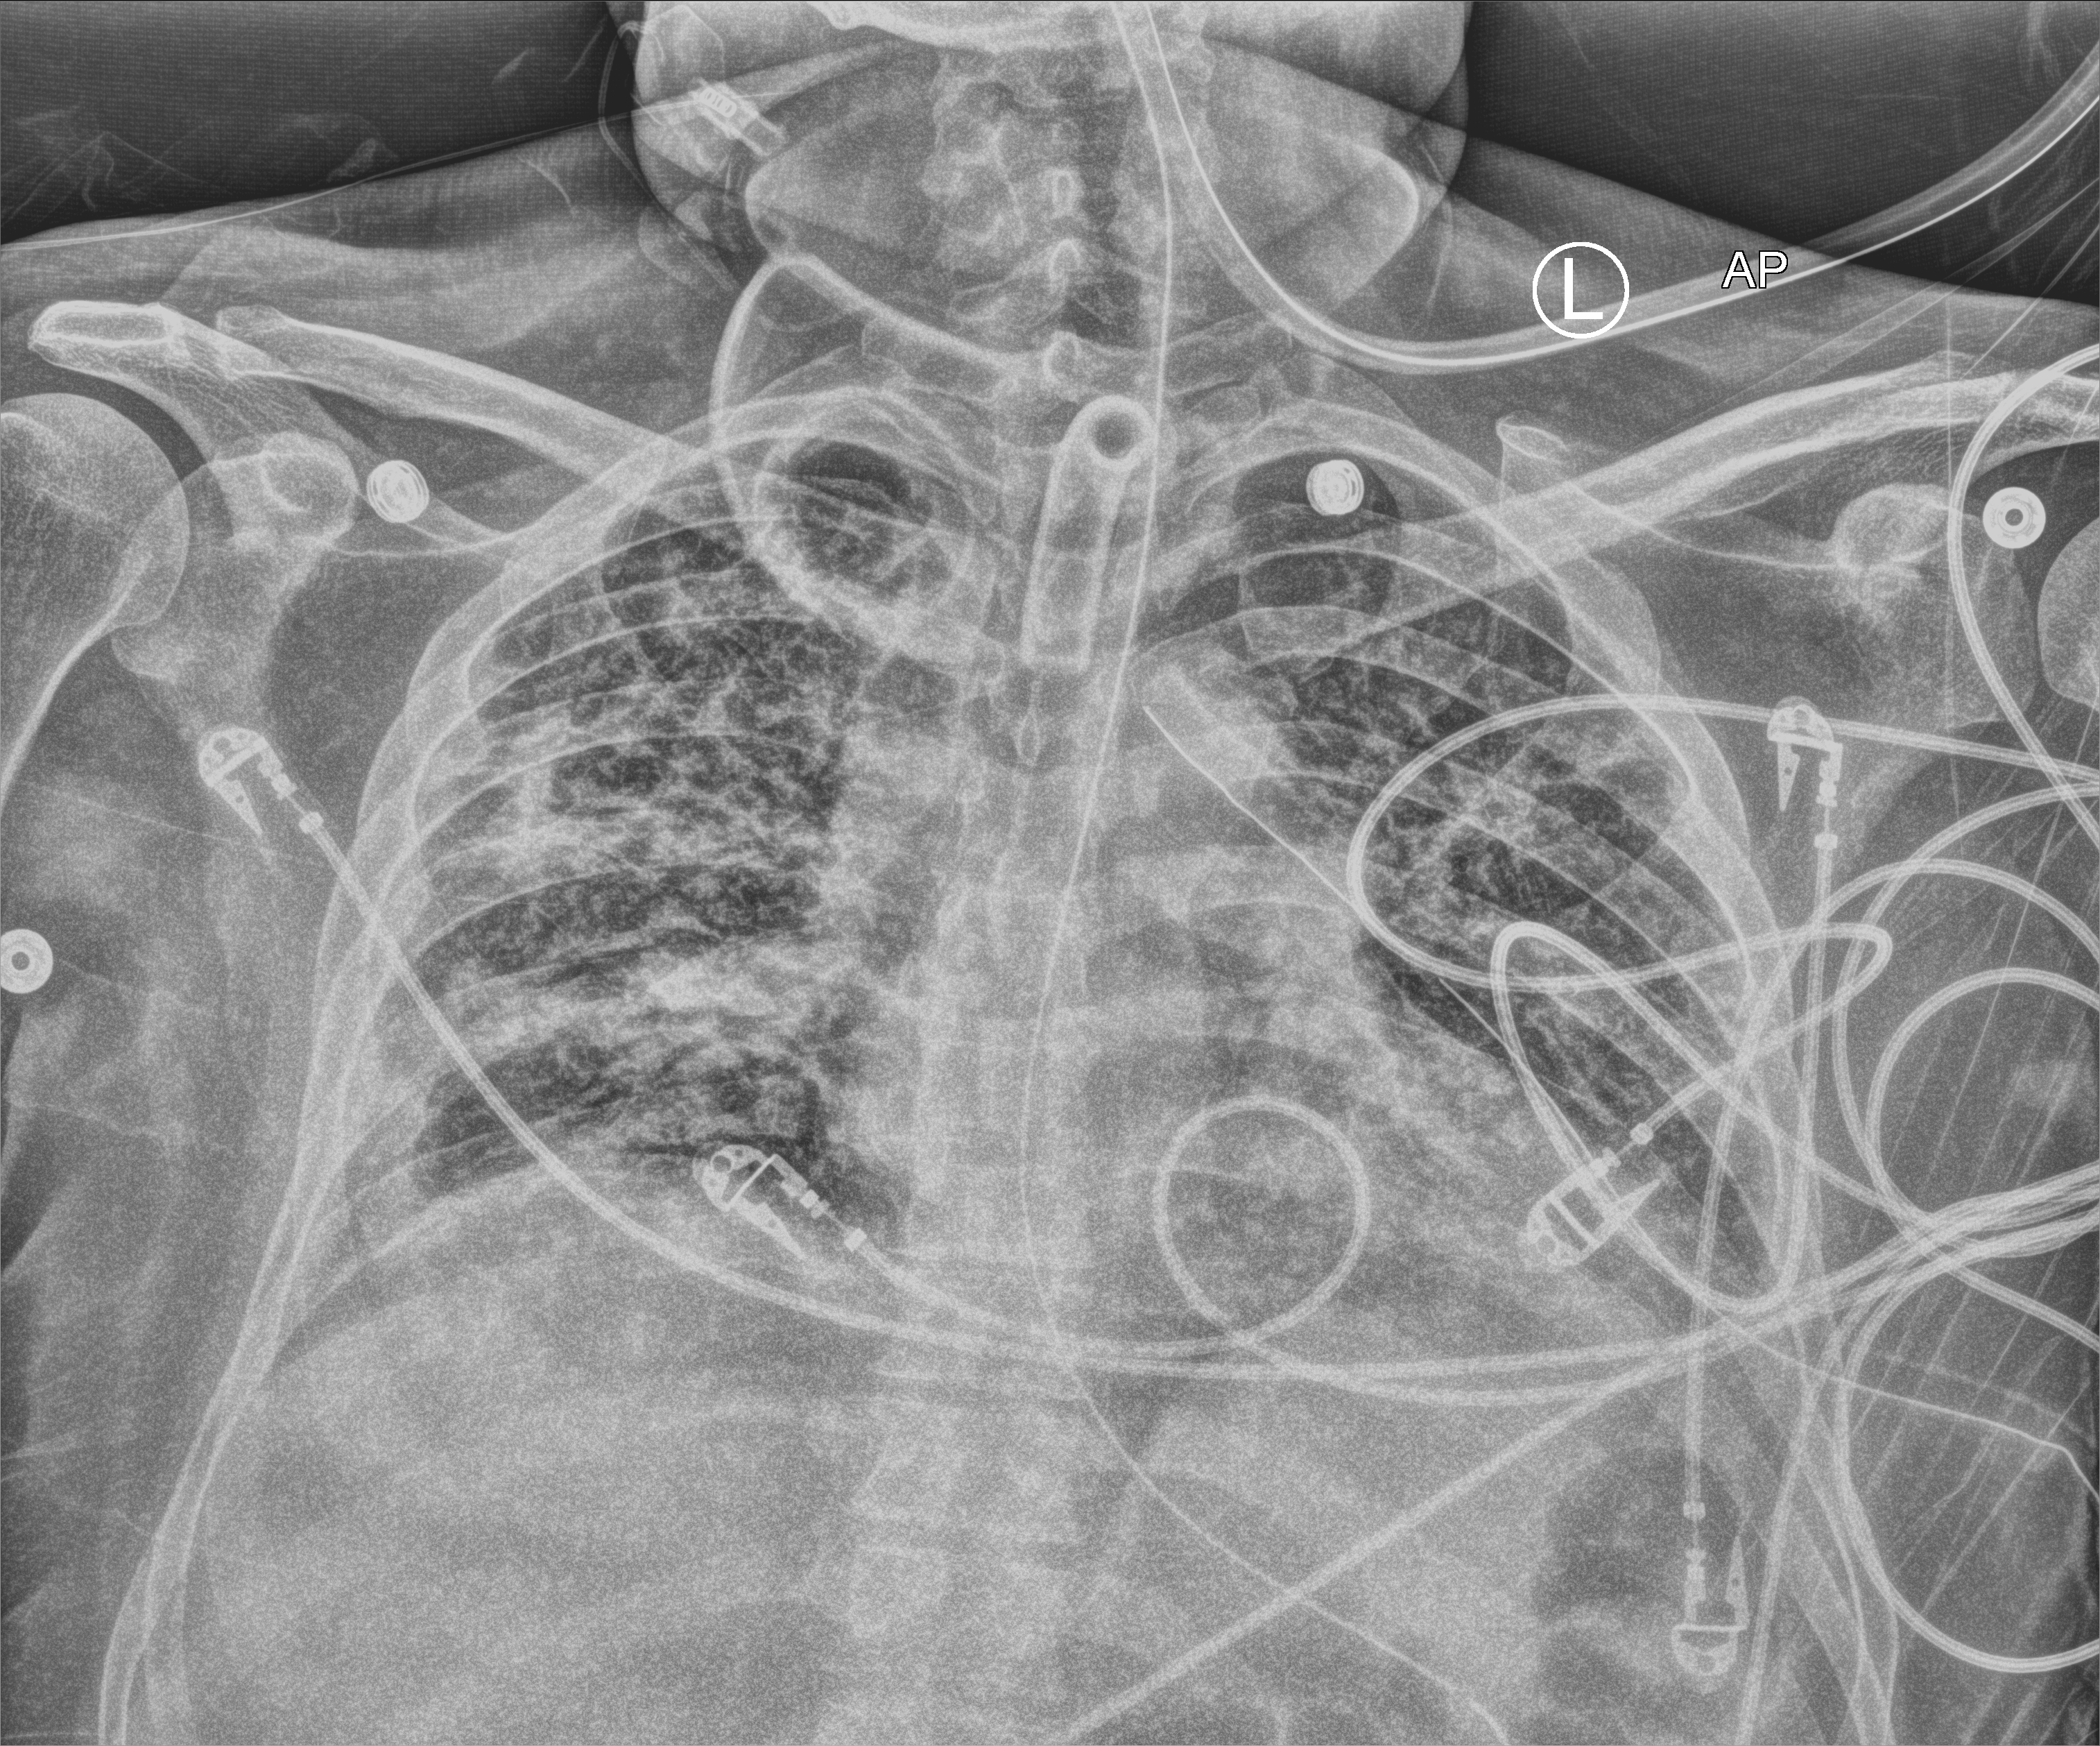
Bedside chest radiograph (computed radiography). Male patient hospitalised with COVID-19, age 18–59 years.
From the hospital-stay record, not from the radiograph (when in the stay this image was taken is not recorded):
- chronic kidney disease (admission record): no